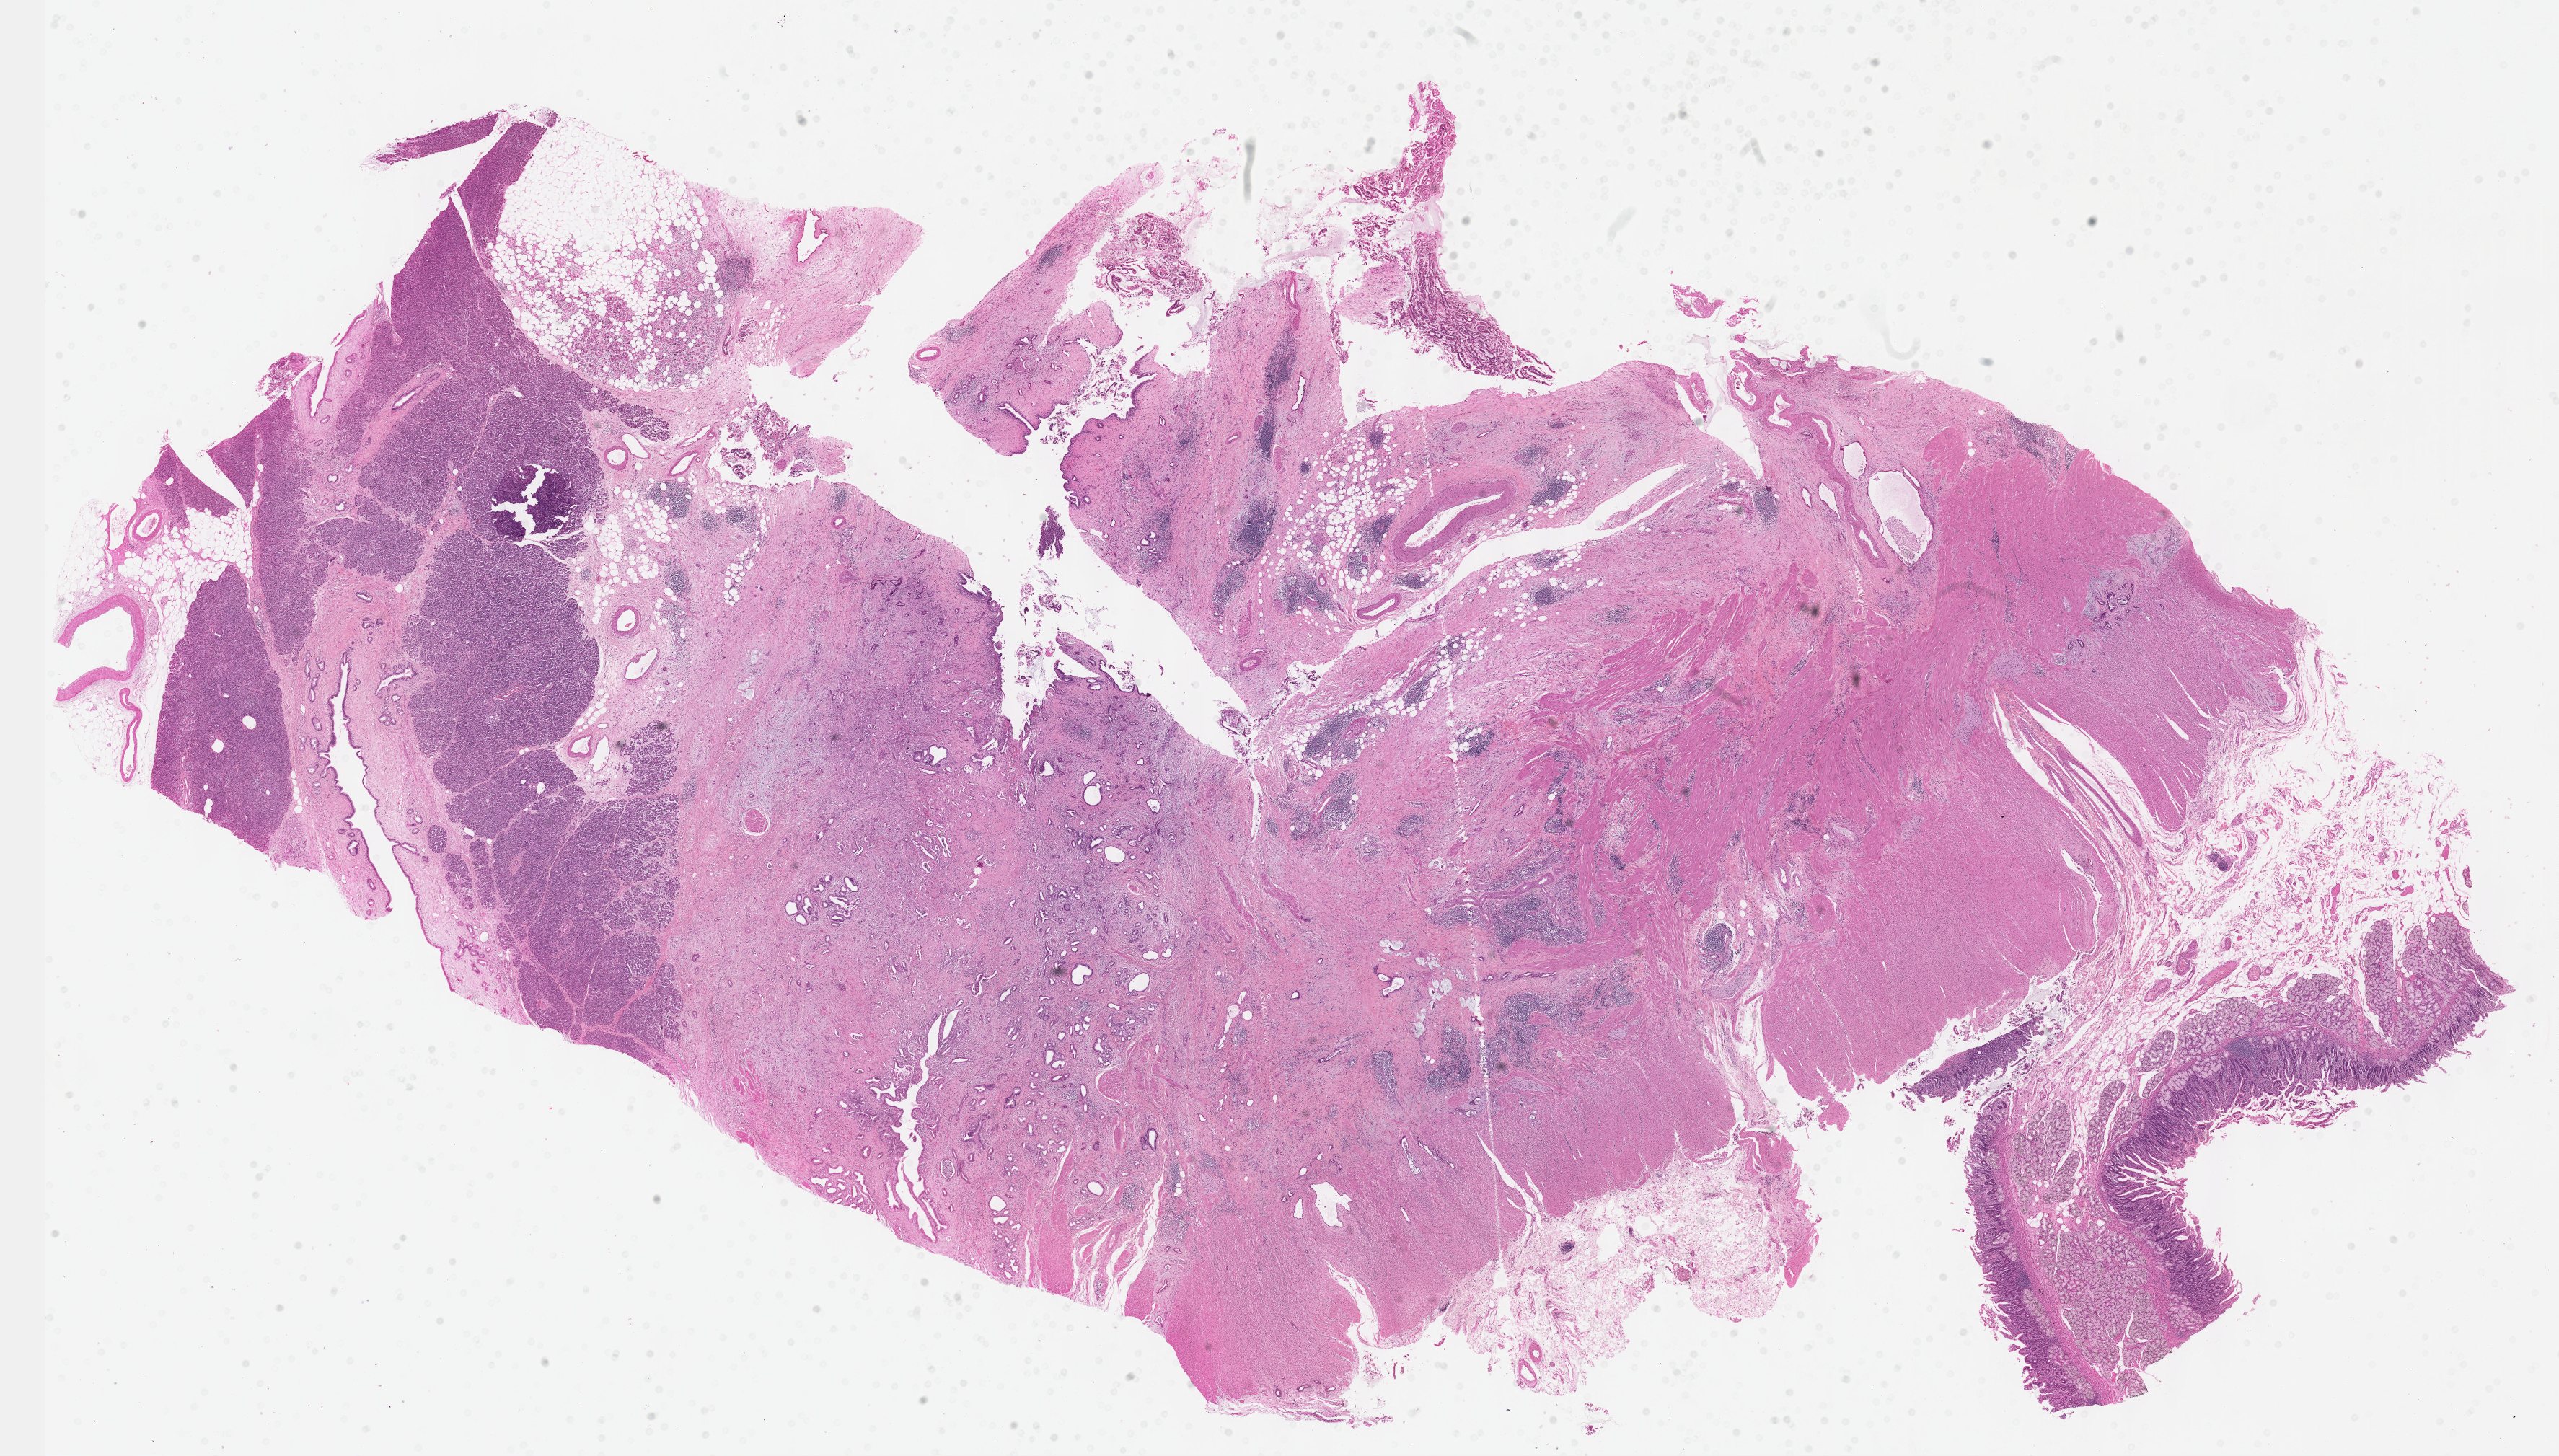
Whole-slide histology image, H&E — low-resolution overview of the scanned area, about 28.7 x 16.3 mm (acquisition: 40x scan); formalin-fixed paraffin-embedded (FFPE) diagnostic section; pancreas, primary tumour sample. Male patient; age at initial diagnosis 73 years. Histologic grade: G3 (poorly differentiated).
TNM: T3 N1 MX. AJCC pathologic stage: IIB. Pathologic diagnosis: Adenocarcinoma, NOS (head of pancreas). Lymph nodes positive (case pathology): 2 of 13 examined.